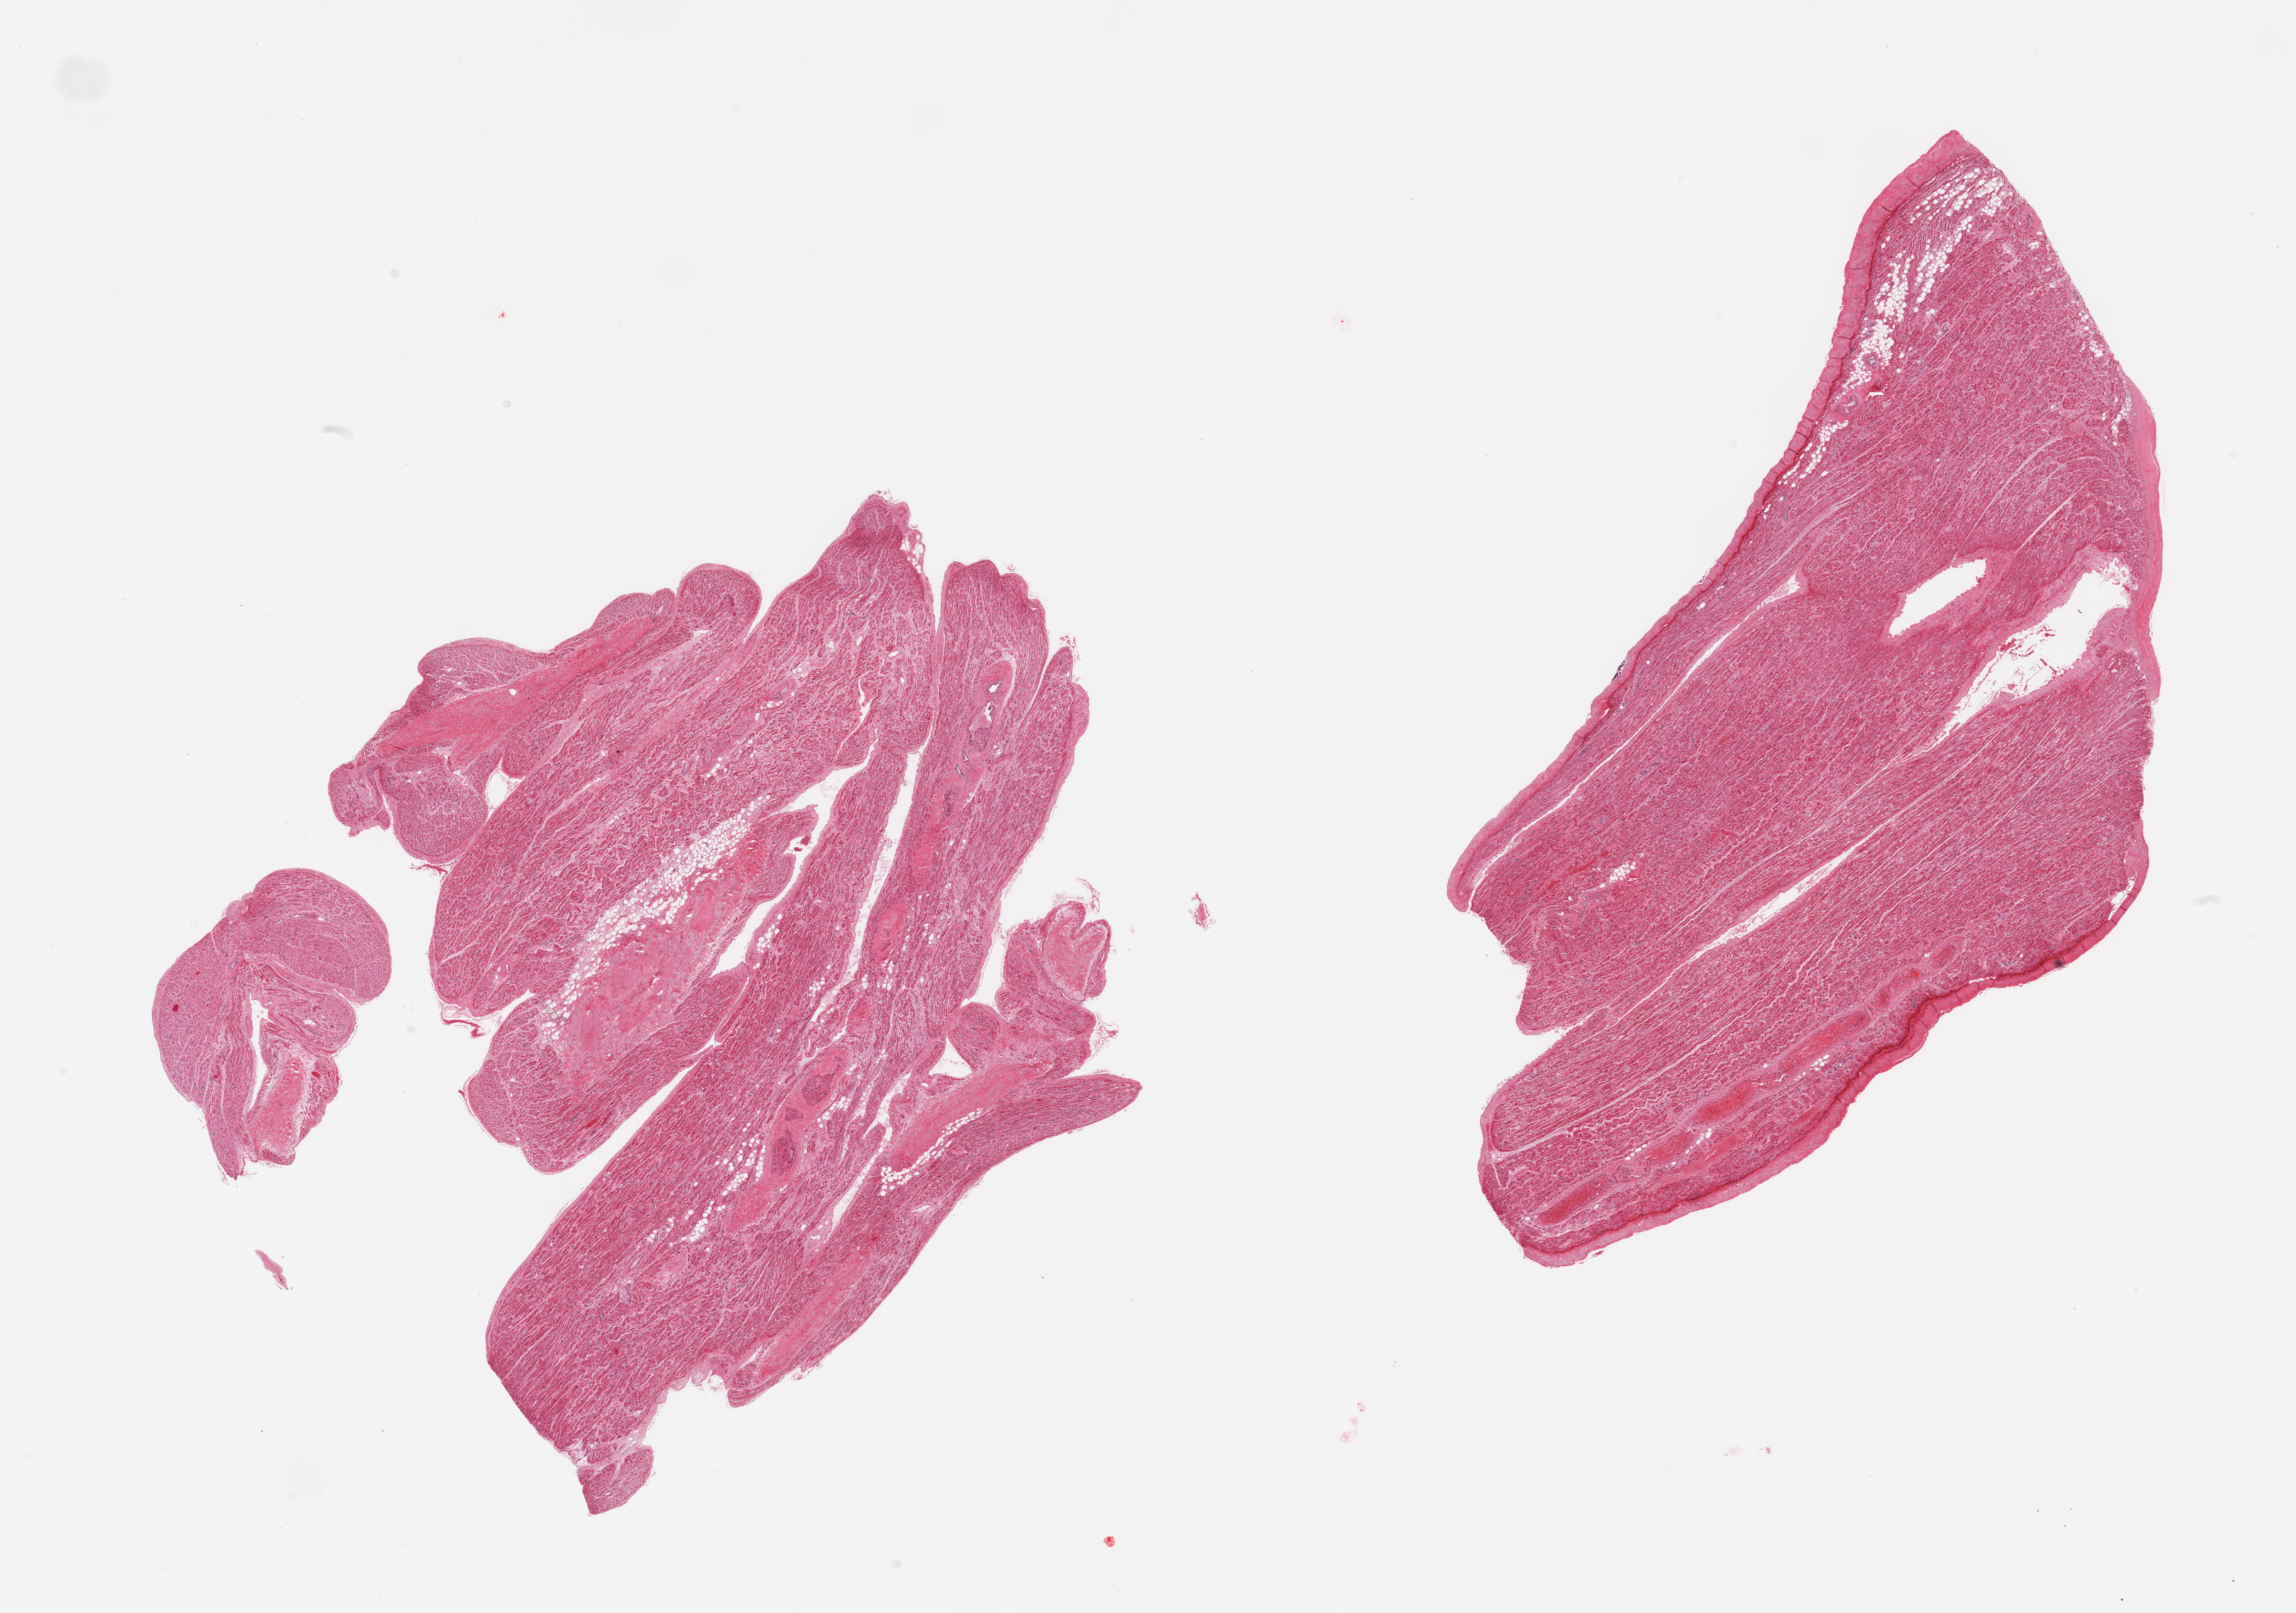
Digitized H&E-stained section, brightfield, whole scanned area (about 25.6 x 18.0 mm, acquisition: 20x scan) shown as a low-resolution overview; PAXgene-fixed, paraffin-embedded tissue; sampled site (target tissue): auricular appendage; donor tissue sample. Donor: male.
Review note (as recorded): 2 pieces.